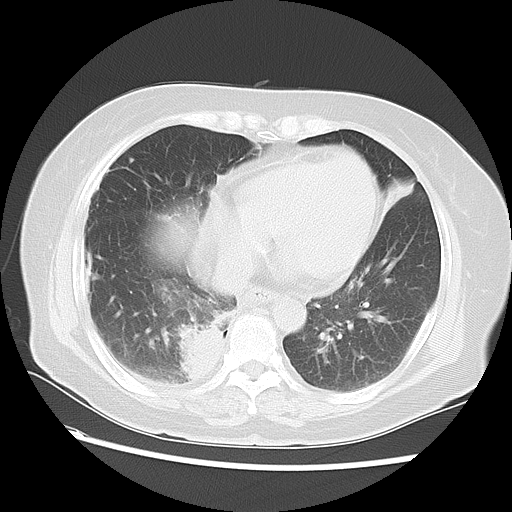
Chest CT, one axial slice; slice 23 of 57 in the series (ordered by position); reconstruction kernel LUNG; 120 kVp; lung window (W 1500 / L -600 HU); 5 mm slice thickness; 512 × 512 image matrix, field of view 350 × 350 mm. Female patient, age 69 years. From the clinical record (not read from this slice): clinical TNM (as recorded): T2 N1 M1a.
Outlined on this slice (rectangle marked by the reading radiologist):
- lung tumour (recorded histology: adenocarcinoma): bounding box [x1, y1, x2, y2] px = [170, 319, 229, 385]